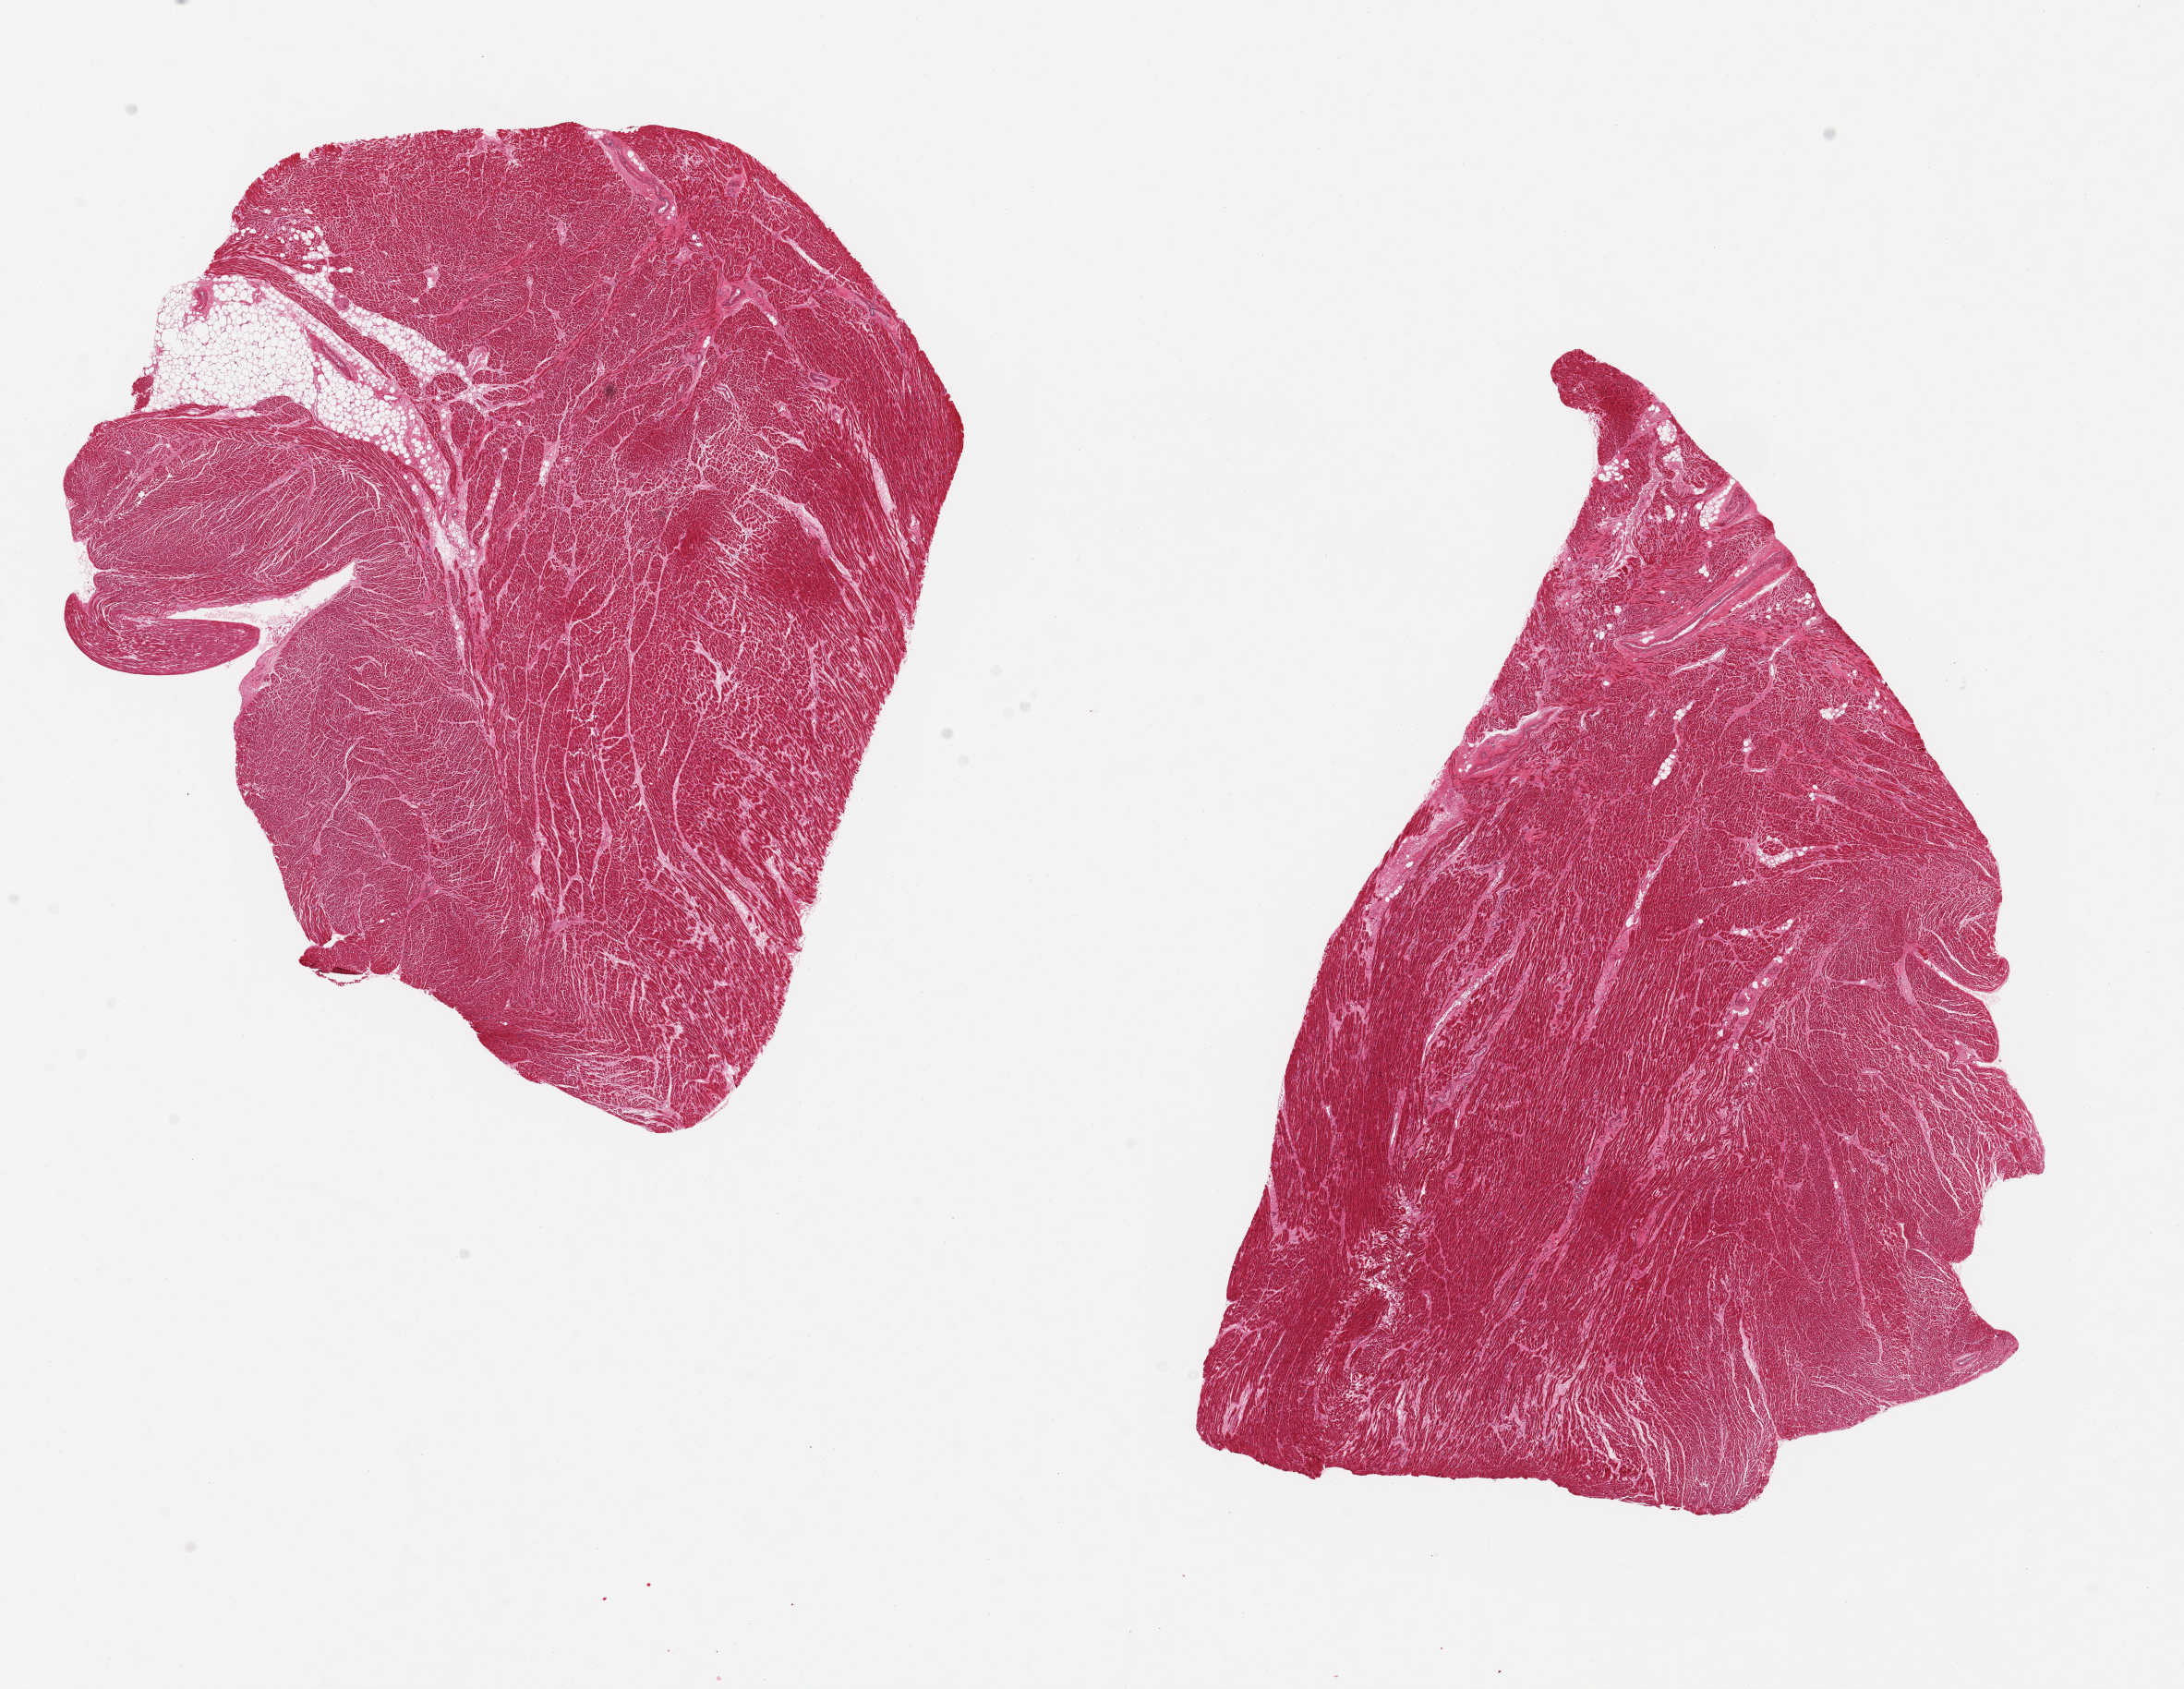
Whole-slide image, hematoxylin and eosin (H&E) stain, brightfield — whole scanned area (about 18.7 x 14.5 mm) shown as a low-resolution overview. PAXgene-fixed, paraffin-embedded tissue. Target tissue: heart. Donor tissue sample. Male donor.
• pathologist's review note for this sample: 2 aliquots, ~9x6mm, mild interstitial fibrosis